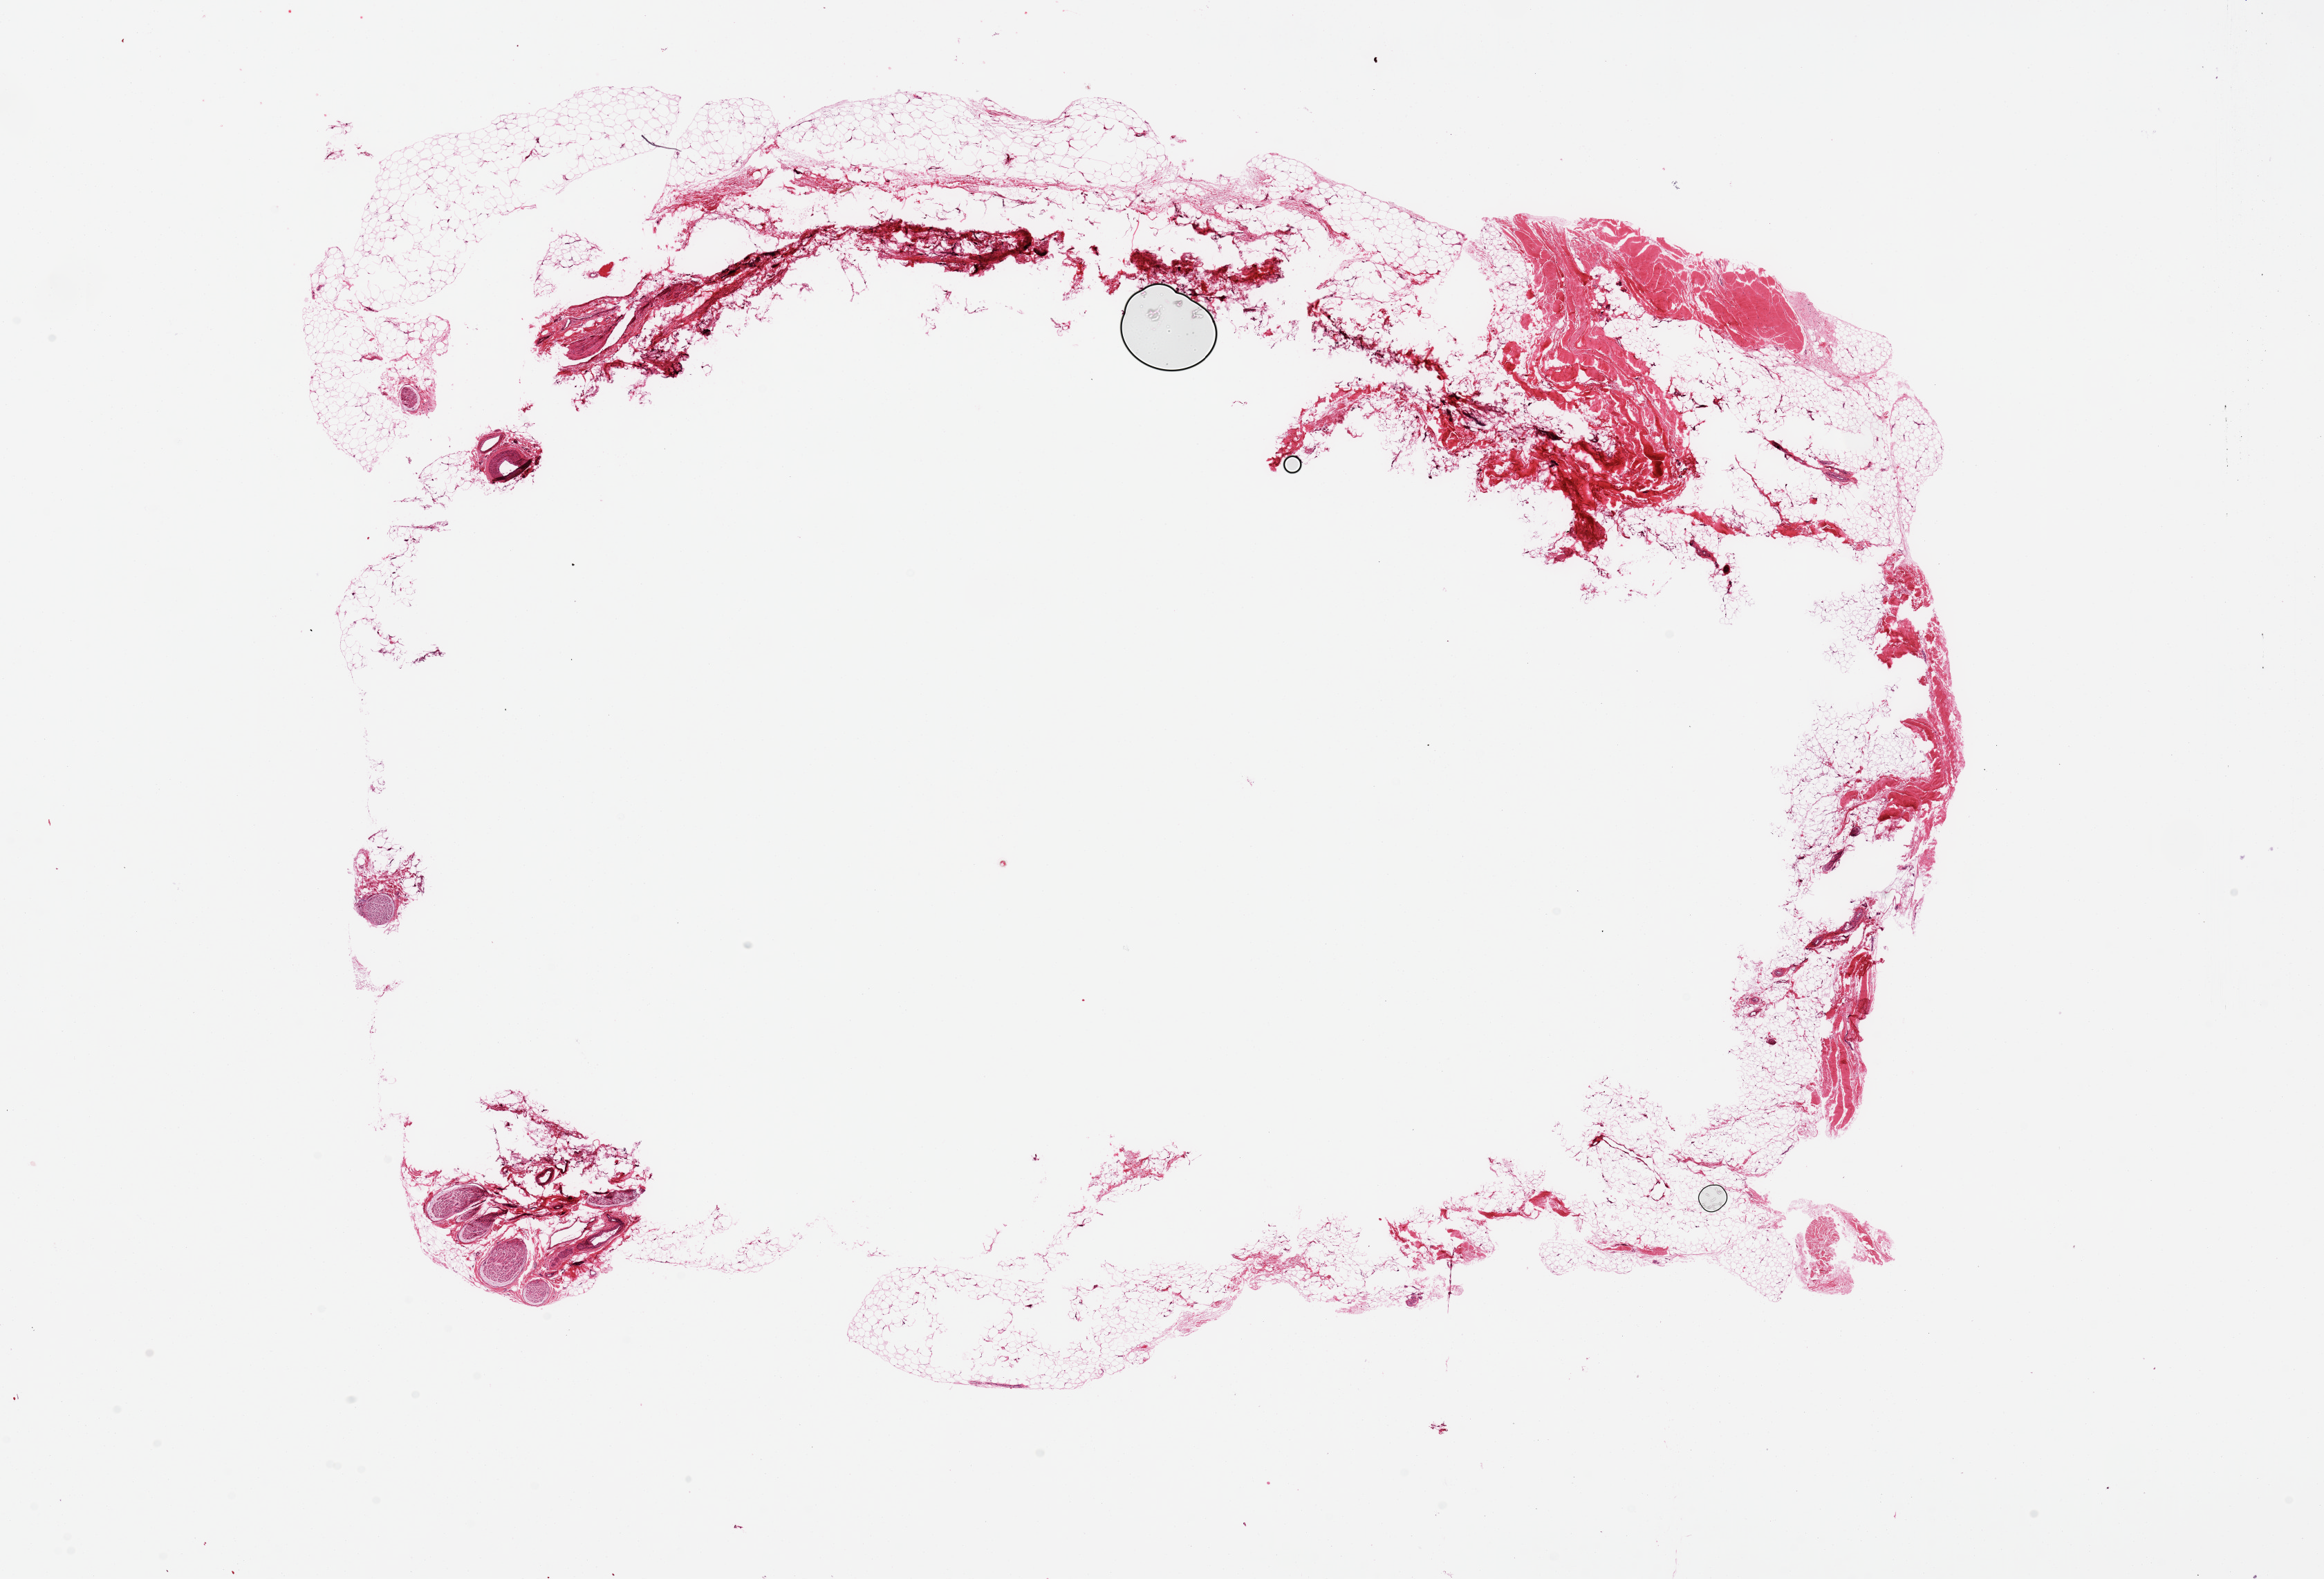
Haematoxylin and eosin whole-slide image, brightfield, whole scanned area (about 26.6 x 18.1 mm, acquisition: 20x scan) shown as a low-resolution overview. PAXgene-fixed paraffin-embedded (PFPE) section. Sampled site (target tissue): adipose tissue. Tissue donor sample. Male donor.
Reviewer comment on this tissue sample: A number of peripheral nerves @ periphery. Large central ???hole???.